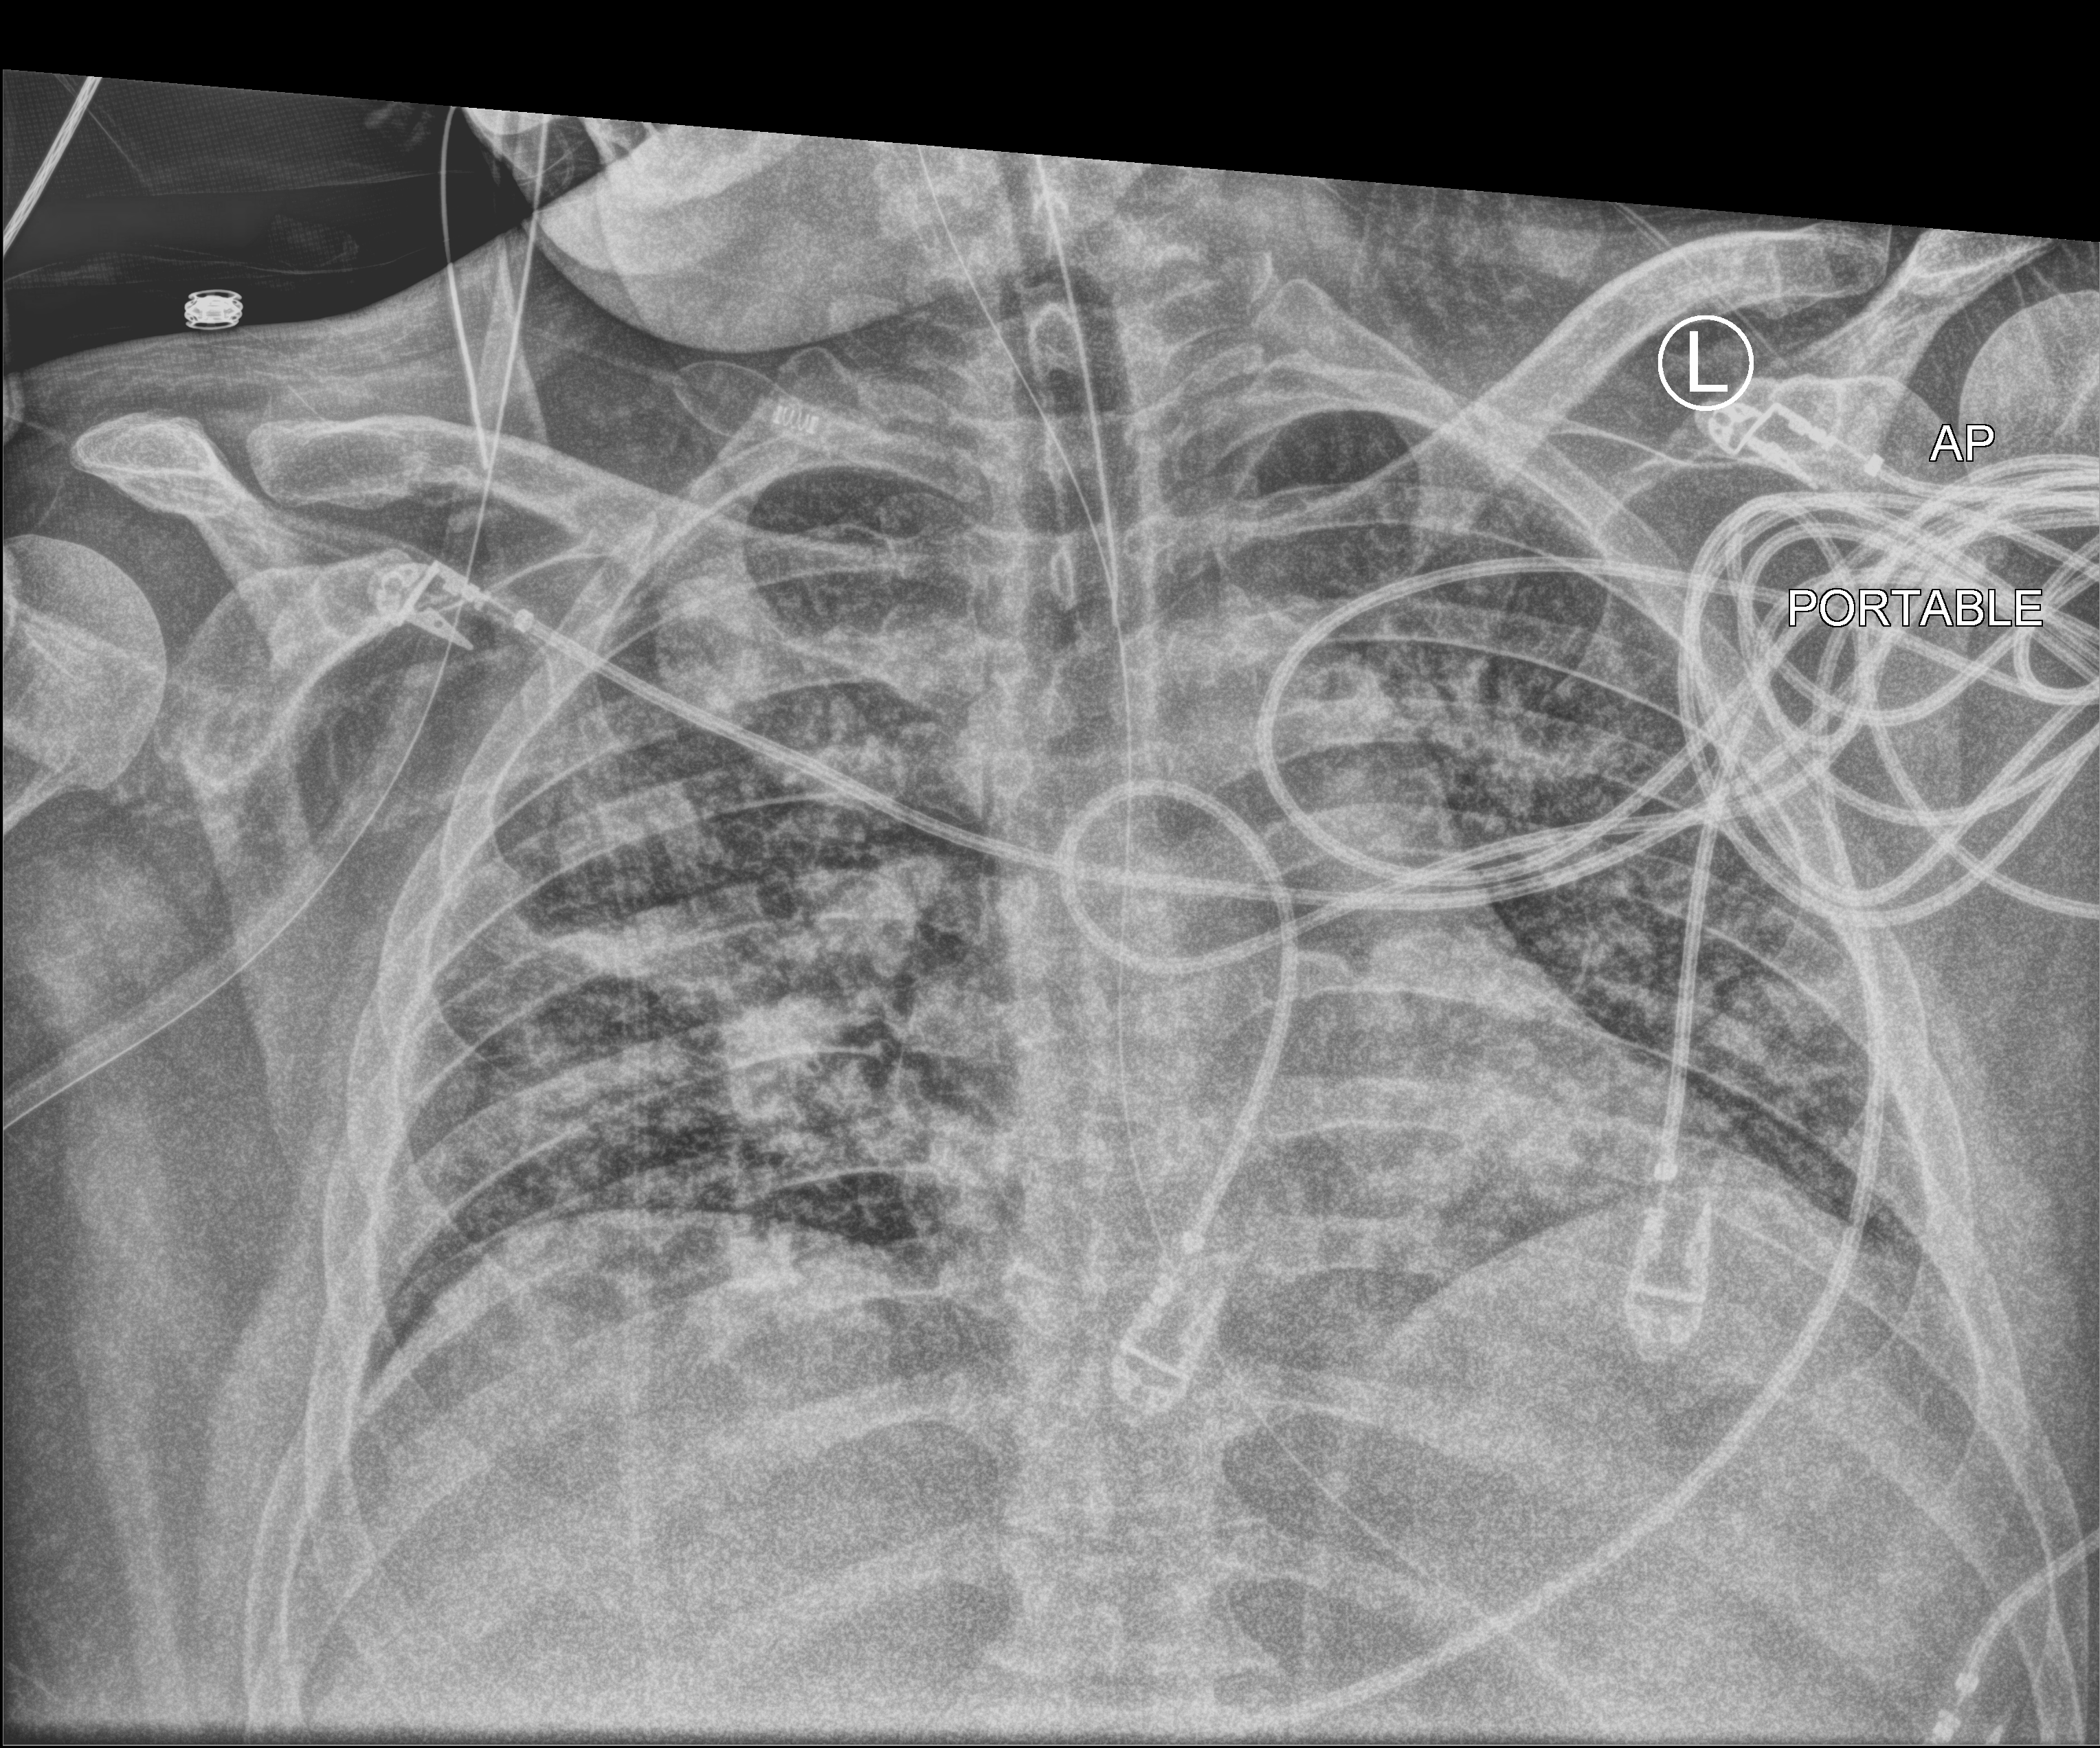
Bedside chest radiograph (computed radiography); anteroposterior (AP) projection. Patient hospitalised with COVID-19, aged 18–59 years.
Hospital-stay facts (about this admission, not read from this image; timing relative to this image not recorded): admitted to intensive care during this hospital stay: yes; mechanically ventilated during this hospital stay: yes.